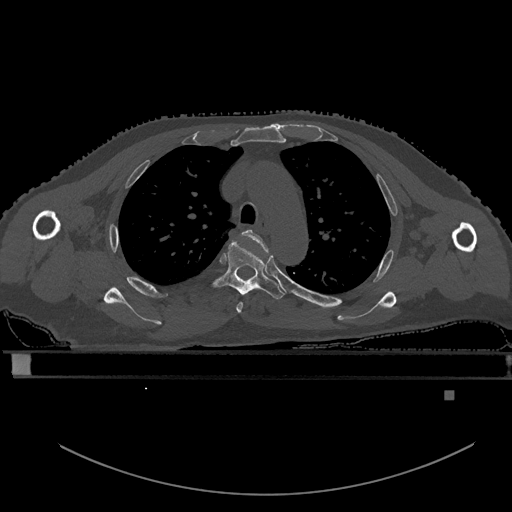
CT including the spine, one axial slice. Slice 415 of 969 in the series (ordered by position). Bone window (W 1800 / L 400 HU). 512 × 512 image matrix. Patient: male, 82 years. Case-level facts recorded for this patient, not image findings: primary cancer: prostate.
Structures marked on this image (semi-automatic segmentation, software-assisted and operator-edited):
- T3 vertebra: bounding box (x1, y1, x2, y2) in pixels: (236, 229, 269, 313)
- T4 vertebra: (214, 239, 285, 300)